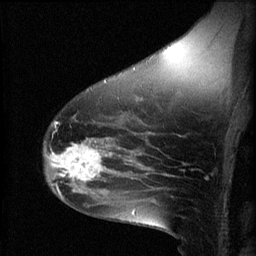
Breast MRI (dynamic contrast-enhanced), one sagittal slice; slice 39 of 60 in the series (ordered by position); 3 images stored at this slice position (order not interpretable as contrast timing); 1.5 T; TE 4.2 ms, TR 8.2 ms; 2 mm slice thickness; 256 × 256 image matrix. Female patient, age 49 years.
Annotated regions visible in this slice (semi-automatically segmented with operator editing):
- analysis volume of interest (the breast-tissue region the enhancement analysis was run in; not a lesion): bounding box [x1, y1, x2, y2] px = [45, 136, 109, 187]
- tumour enhancement mask (voxels above the 70 % enhancement threshold inside the analysis volume of interest): [47, 140, 109, 187]